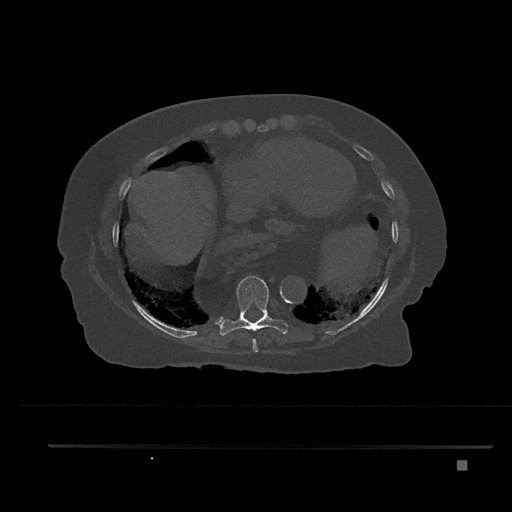
CT including the spine, one axial slice; position 403 of 797 along the scan axis; bone window (W 1800 / L 400 HU); 512 × 512 image matrix, field of view 437 × 437 mm. Female patient, age 76 years. Case-level facts recorded for this patient, not image findings: primary cancer: lung; vertebrae with lytic lesions (as recorded): T11, L3.
Outlined on this slice (semi-automatically segmented with operator editing):
- T8 vertebra: bounding box (x1, y1, x2, y2) in pixels: (252, 338, 258, 353)
- T9 vertebra: (216, 276, 288, 336)